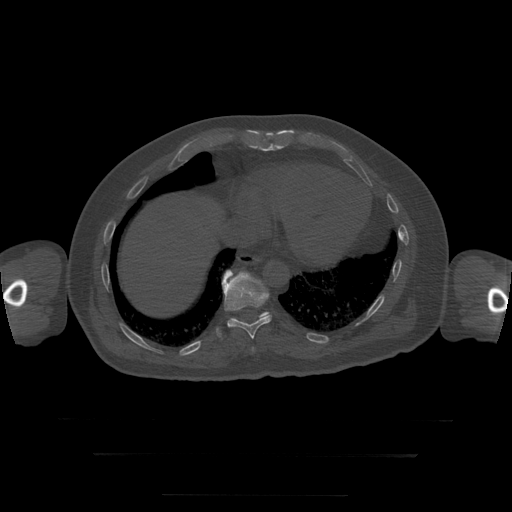
CT including the spine, one axial slice; position 119 of 397 along the scan axis; reconstruction kernel STANDARD; bone window (W 1800 / L 400 HU); 1.25 mm slice thickness; 512 × 512 image matrix, field of view 510 × 510 mm. Patient age 73 years. From the clinical record (not read from this slice): primary cancer: prostate.
Structures marked on this image (semi-automatically segmented with operator editing):
- T10 vertebra: bounding box (x1, y1, x2, y2) in pixels: (217, 270, 272, 339)
- T11 vertebra: (234, 312, 269, 320)
- T9 vertebra: (252, 348, 254, 351)